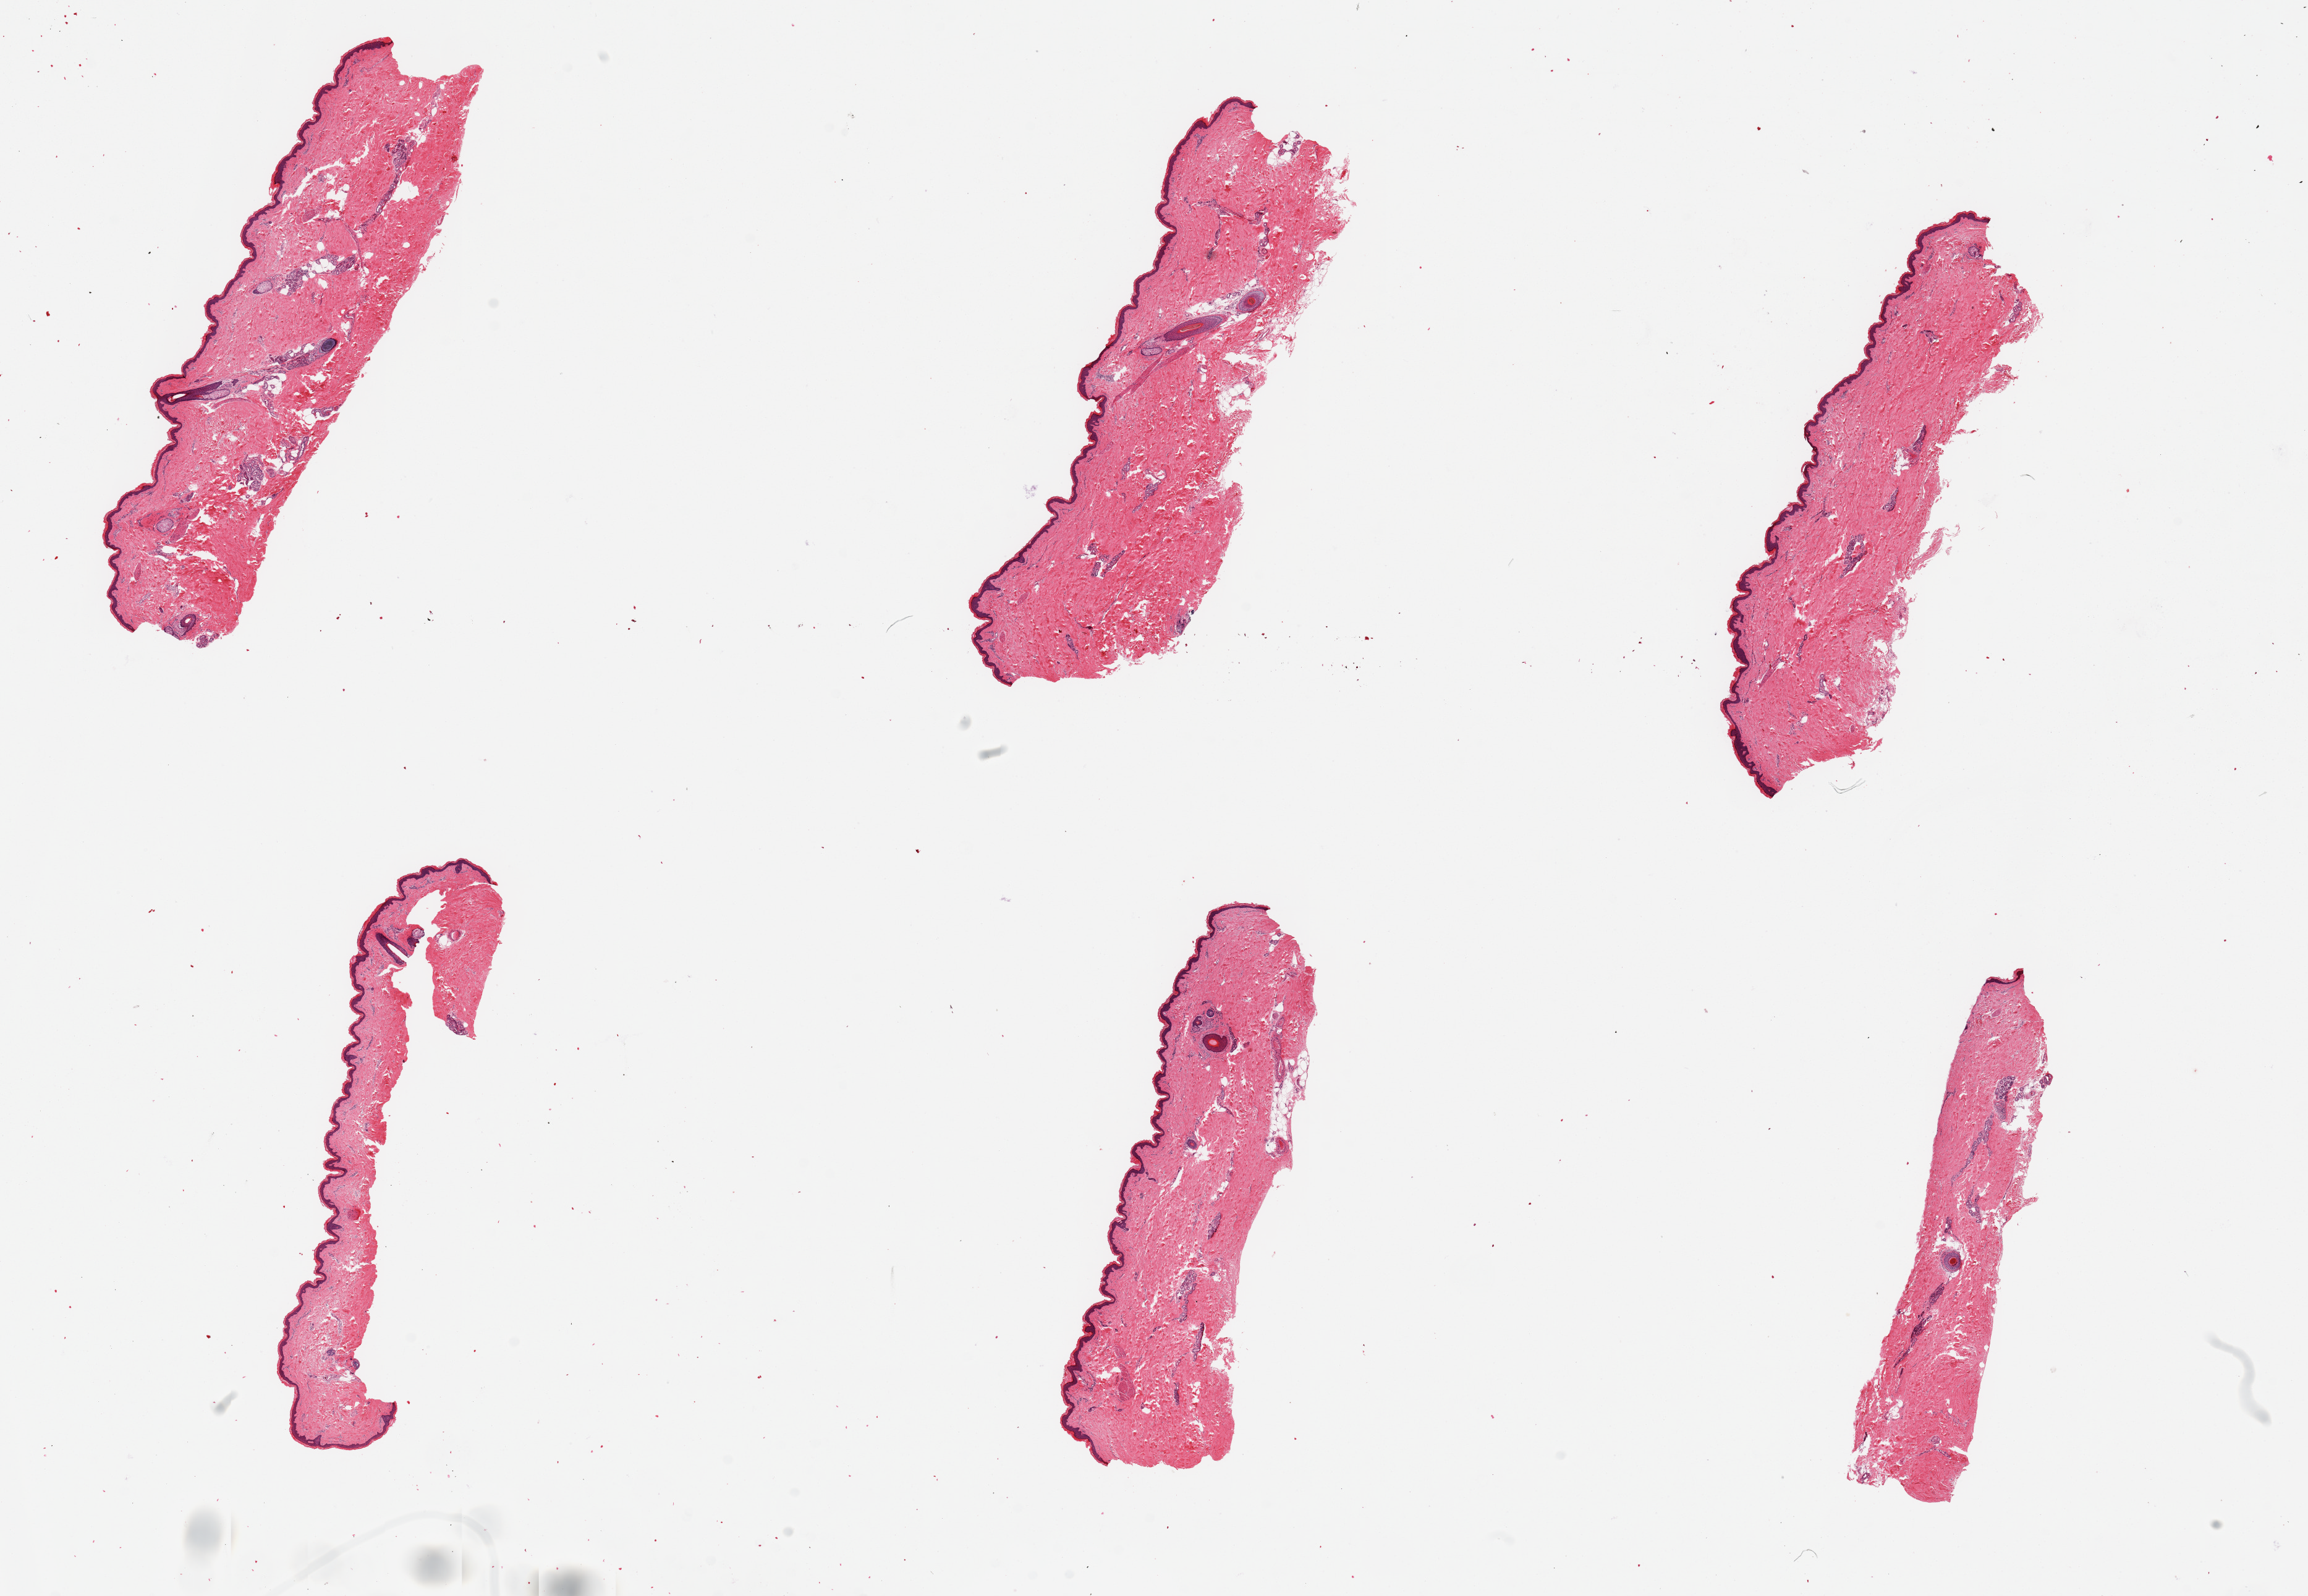
Digitized hematoxylin and eosin (H&E)-stained section, whole scanned area (about 29.5 x 20.4 mm, slide scanned at 20x) shown as a low-resolution overview, PAXgene-fixed, paraffin-embedded tissue, sampled site (target tissue): skin of lower leg, donor tissue sample. Male donor.
- reviewer comment on this tissue sample: 6 pieces ~7x2mm. Squamous epithelium is 2-3% thickness